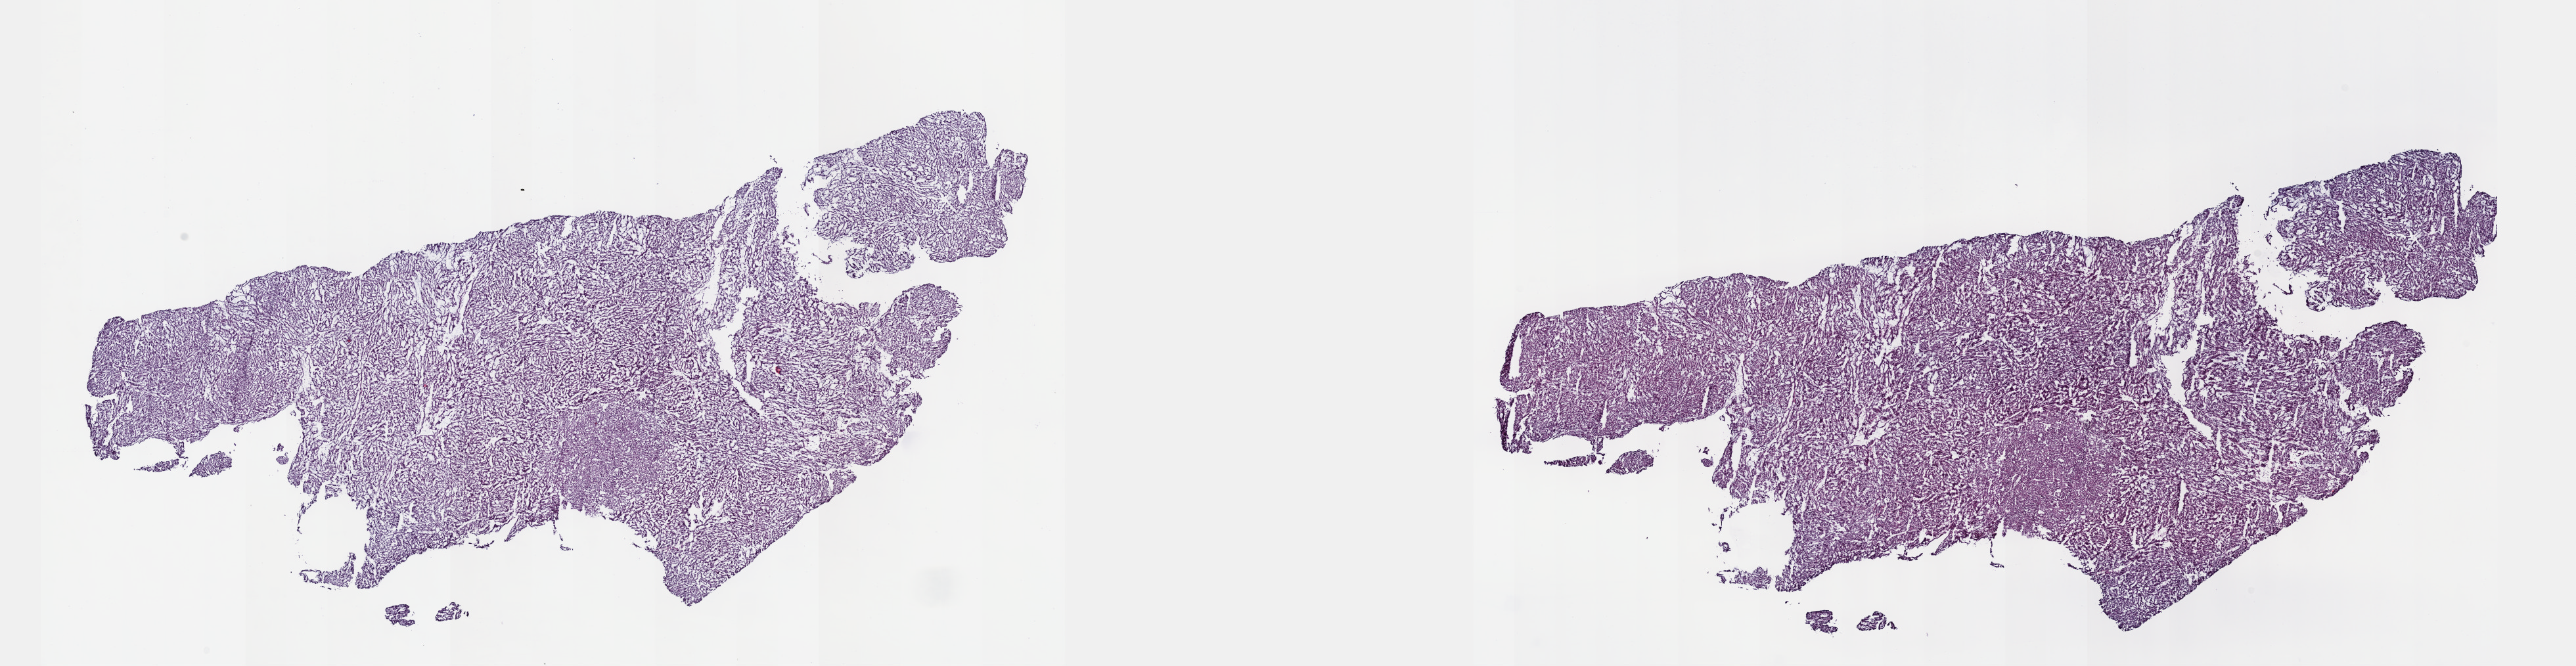
H&E whole-slide image — shown as a low-resolution overview of the whole scanned area (about 31.7 x 8.2 mm). Frozen section from the top of the tissue portion. Kidney, primary tumour sample. Female patient; age at initial diagnosis 76 years. Pathologist review of this section (percent, as recorded): tumour cells 93%, tumour nuclei 96%, normal cells 0%, stromal cells 5%, necrosis 2%. Inflammatory infiltration, as recorded: lymphocyte infiltration 2%, monocyte infiltration 1%, neutrophil infiltration 0%.
- TNM: T1b N0 MX
- AJCC pathologic stage: I
- diagnosis: Papillary adenocarcinoma, NOS